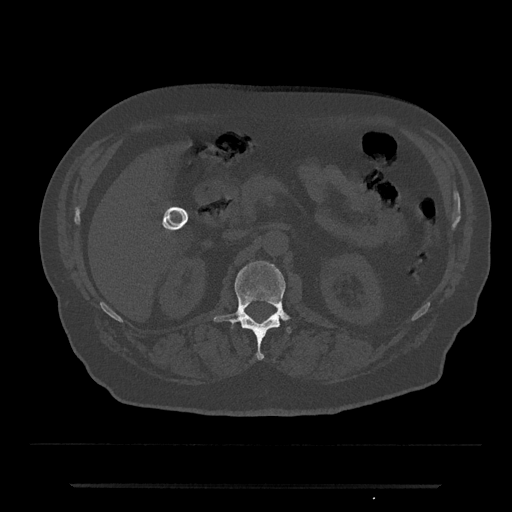
CT including the spine, one axial slice. Position 532 of 797 along the scan axis. Reconstruction kernel Br40s/3. 120 kVp. Bone window (W 1800 / L 400 HU). 0.5 mm slice thickness. 512 × 512 image matrix, field of view 434 × 434 mm. Patient: male, 80 years. From the clinical record (not read from this slice): primary cancer: prostate; vertebrae with lytic lesions (as recorded): L1, T11.
Structures marked on this image (semi-automatic segmentation, software-assisted and operator-edited):
- L1 vertebra: box from (x=214, y=260) to (x=290, y=360) px